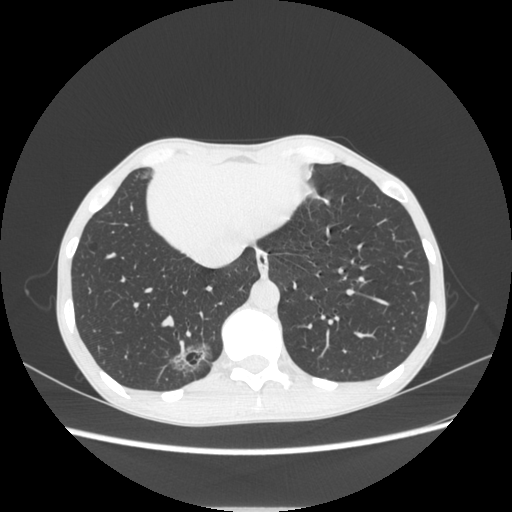
Chest CT, one axial slice; position 72 of 272 along the scan axis; lung window (W 1500 / L -600 HU); 1.25 mm slice thickness; 512 × 512 image matrix. Patient: female, 51 years. Case-level facts recorded for this patient, not image findings: clinical TNM (as recorded): T1c N0 M0.
Structures marked on this image (rectangle marked by the reading radiologist):
- lung tumour (recorded histology: adenocarcinoma): box from (x=165, y=336) to (x=222, y=383) px